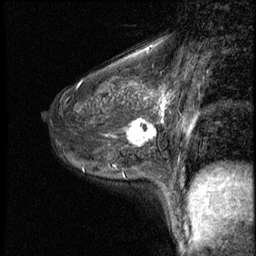
Breast MRI (dynamic contrast-enhanced), one sagittal slice. Position 35 of 50 along the scan axis. 3 images stored at this slice position (order not interpretable as contrast timing). 1.5 T. TE 4.2 ms, TR 8.7 ms. 256 × 256 image matrix, field of view 180 × 180 mm. Patient: female, 43 years. From the clinical record (not read from this slice): setting: breast cancer imaged before/during neoadjuvant chemotherapy; receptor status: HR-positive, HER2-negative.
Structures marked on this image (semi-automatic segmentation, software-assisted and operator-edited):
- analysis volume of interest (the breast-tissue region the enhancement analysis was run in; not a lesion): bounding box <122,109,159,155> (left, top, right, bottom; pixels)
- tumour enhancement mask (voxels above the 140 % enhancement threshold inside the analysis volume of interest): <127,119,156,145>